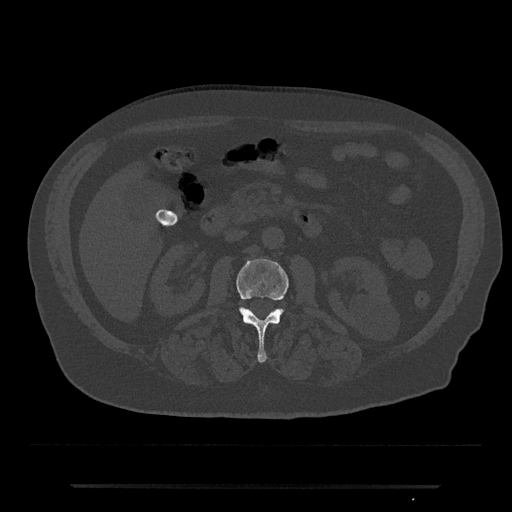
CT including the spine, one axial slice. Position 466 of 797 along the scan axis. 120 kVp. Bone window (W 1800 / L 400 HU). 0.5 mm slice thickness. 512 × 512 image matrix, field of view 434 × 434 mm. Male patient, age 80 years. Case-level facts recorded for this patient, not image findings: primary cancer: prostate; vertebrae with lytic lesions (as recorded): L1, T11.
Outlined on this slice (semi-automatically segmented with operator editing):
- L2 vertebra: bounding box <236,259,289,363> (left, top, right, bottom; pixels)